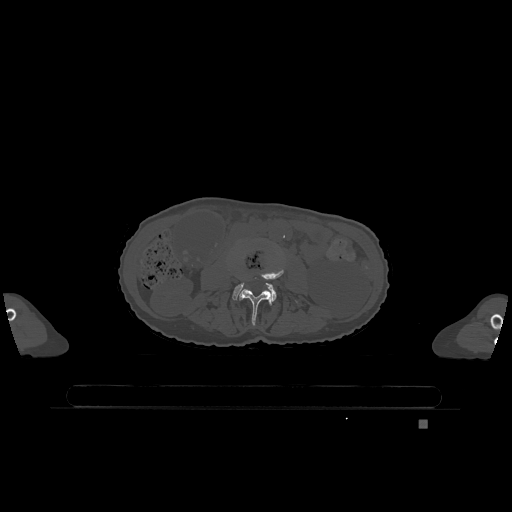
CT including the spine, one axial slice. Slice 340 of 1317 in the series (ordered by position). Bone window (W 1800 / L 400 HU). 512 × 512 image matrix, field of view 500 × 500 mm. Female patient, age 74 years. Case-level facts recorded for this patient, not image findings: primary cancer: lung; vertebrae with lytic lesions (as recorded): T1, T4, T5, T6, L4, L5.
Structures marked on this image (semi-automatic segmentation, software-assisted and operator-edited):
- L3 vertebra: bounding box (x1, y1, x2, y2) in pixels: (238, 268, 298, 325)
- L4 vertebra: (232, 282, 277, 302)